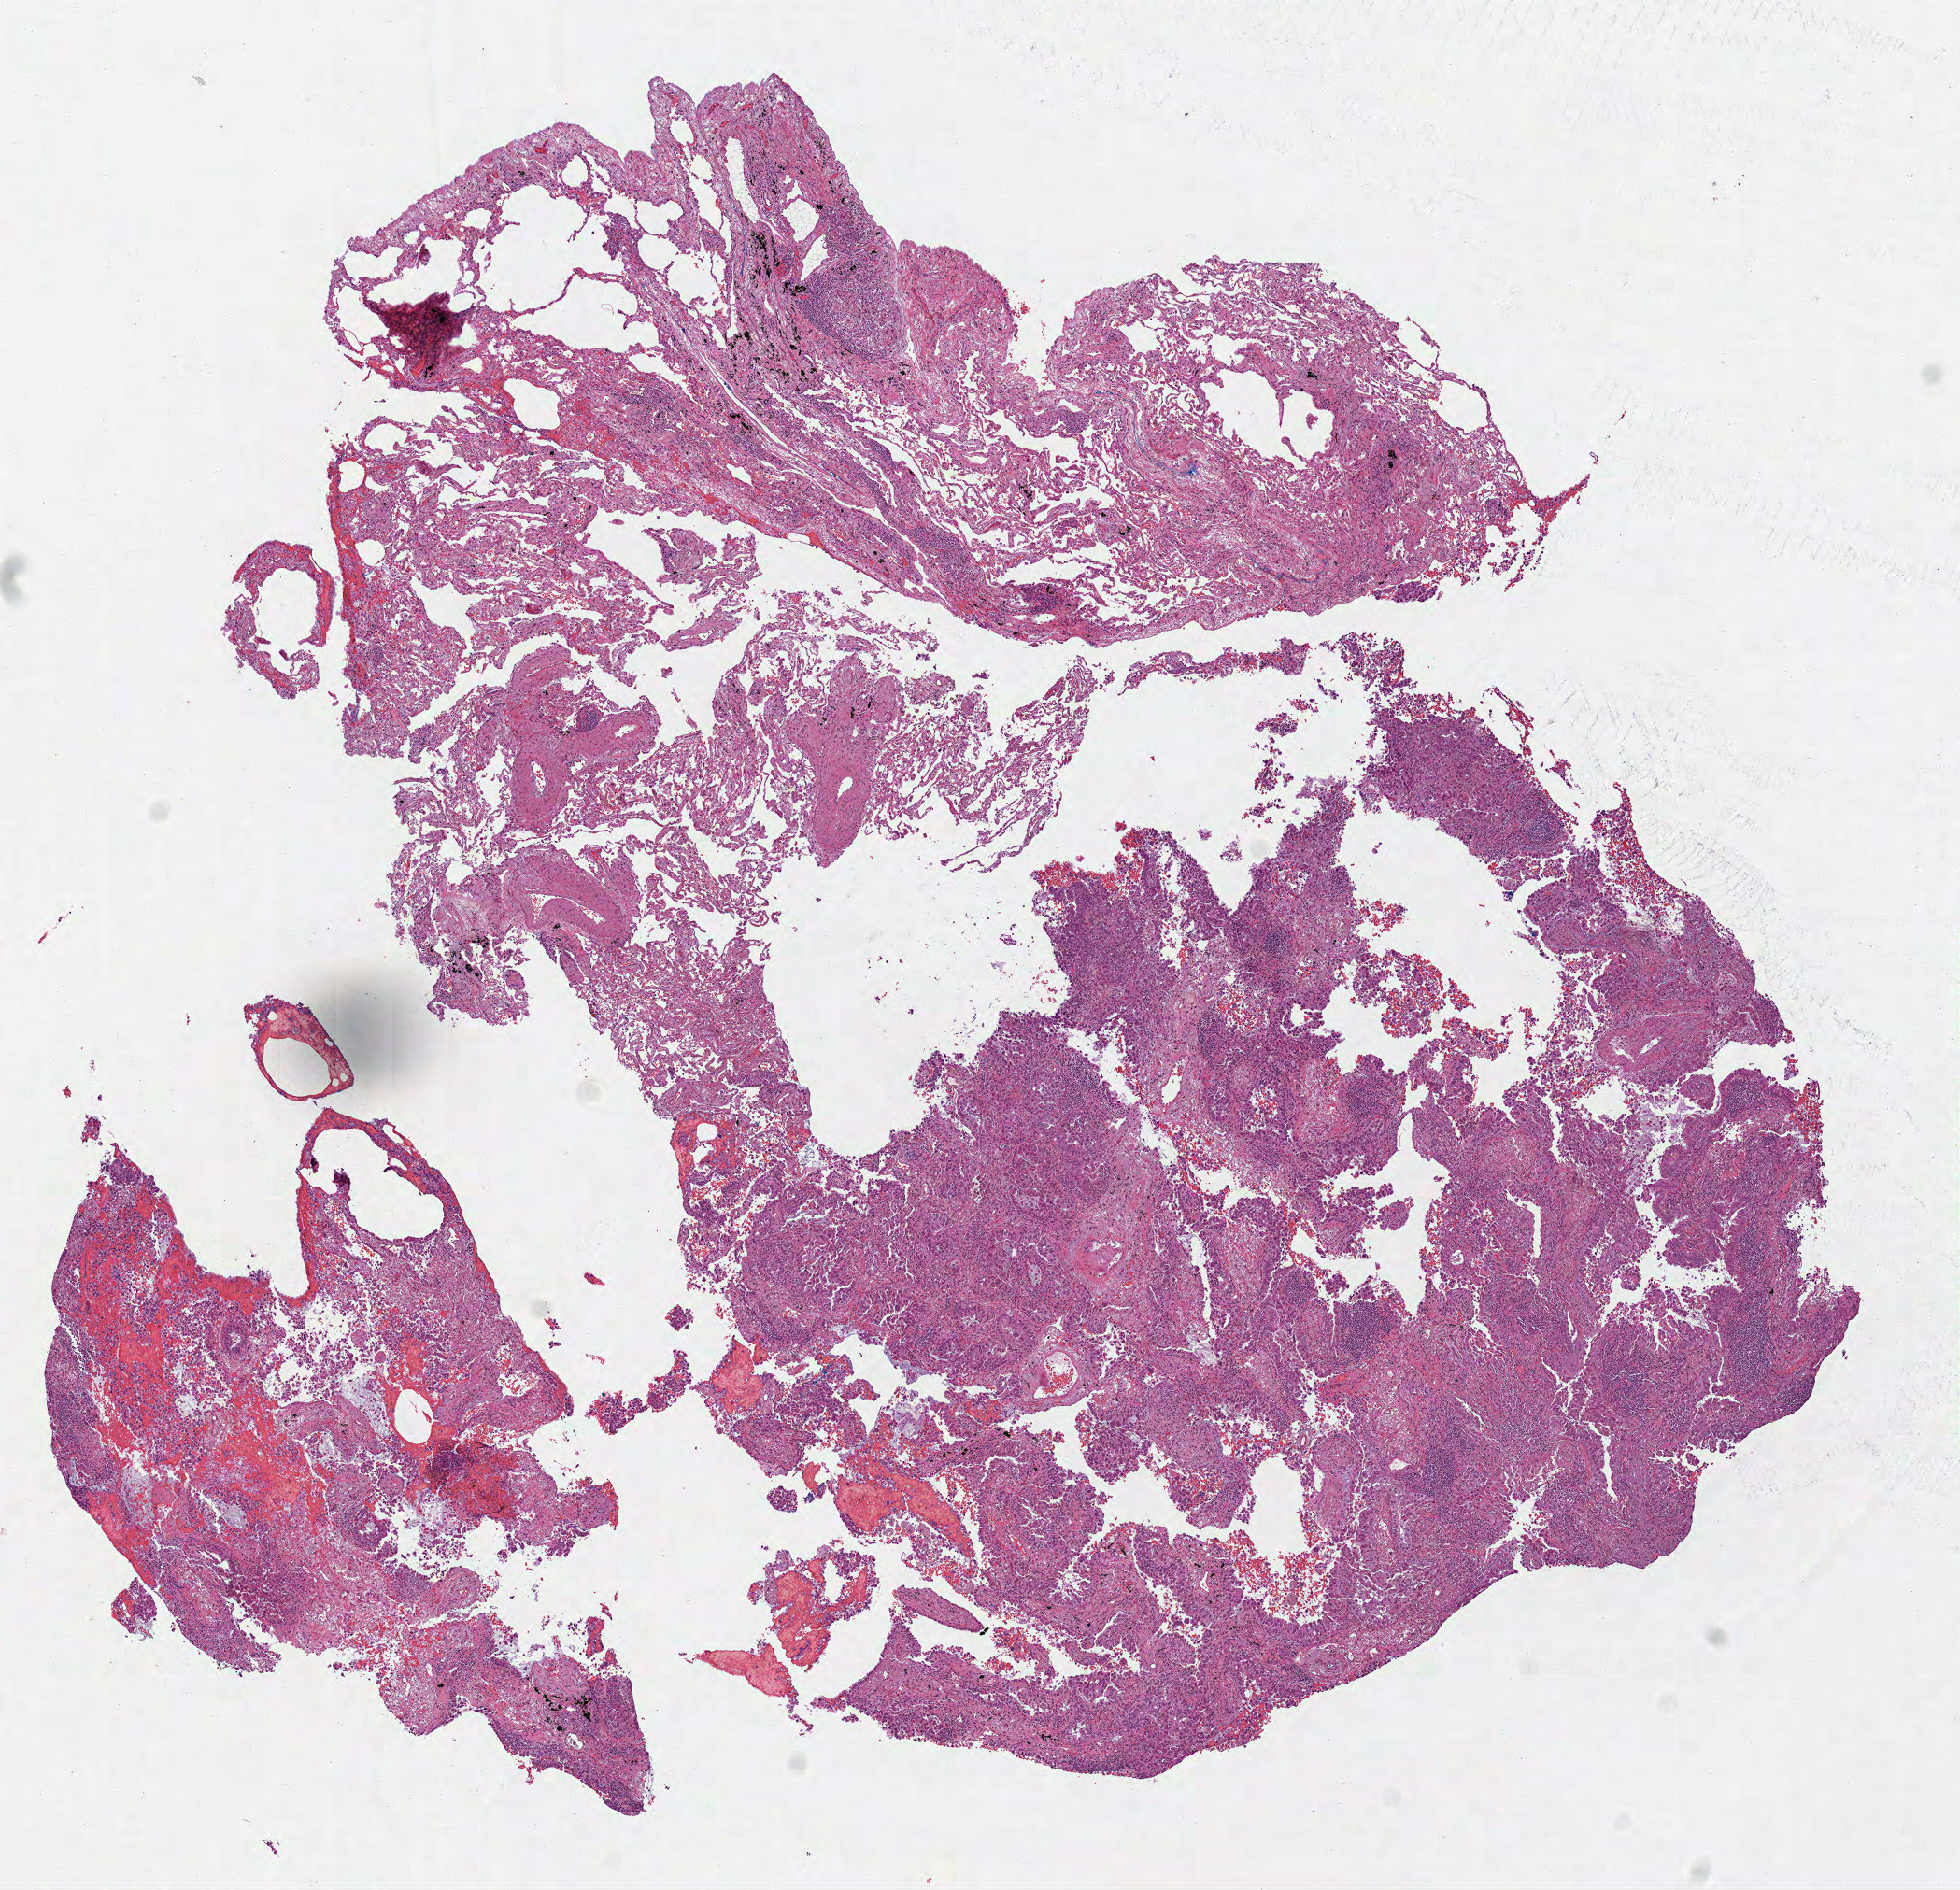
Digitized Hematoxylin and eosin (H&E) stained tissue section (whole slide) — whole scanned area (about 8.5 x 8.2 mm) shown as a low-resolution overview; formalin-fixed paraffin-embedded (FFPE) diagnostic section; lung, primary tumour sample. Female, age 81 years at initial diagnosis.
* histologic diagnosis: Adenocarcinoma, NOS (lower lobe, lung)
* AJCC pathologic stage: IA